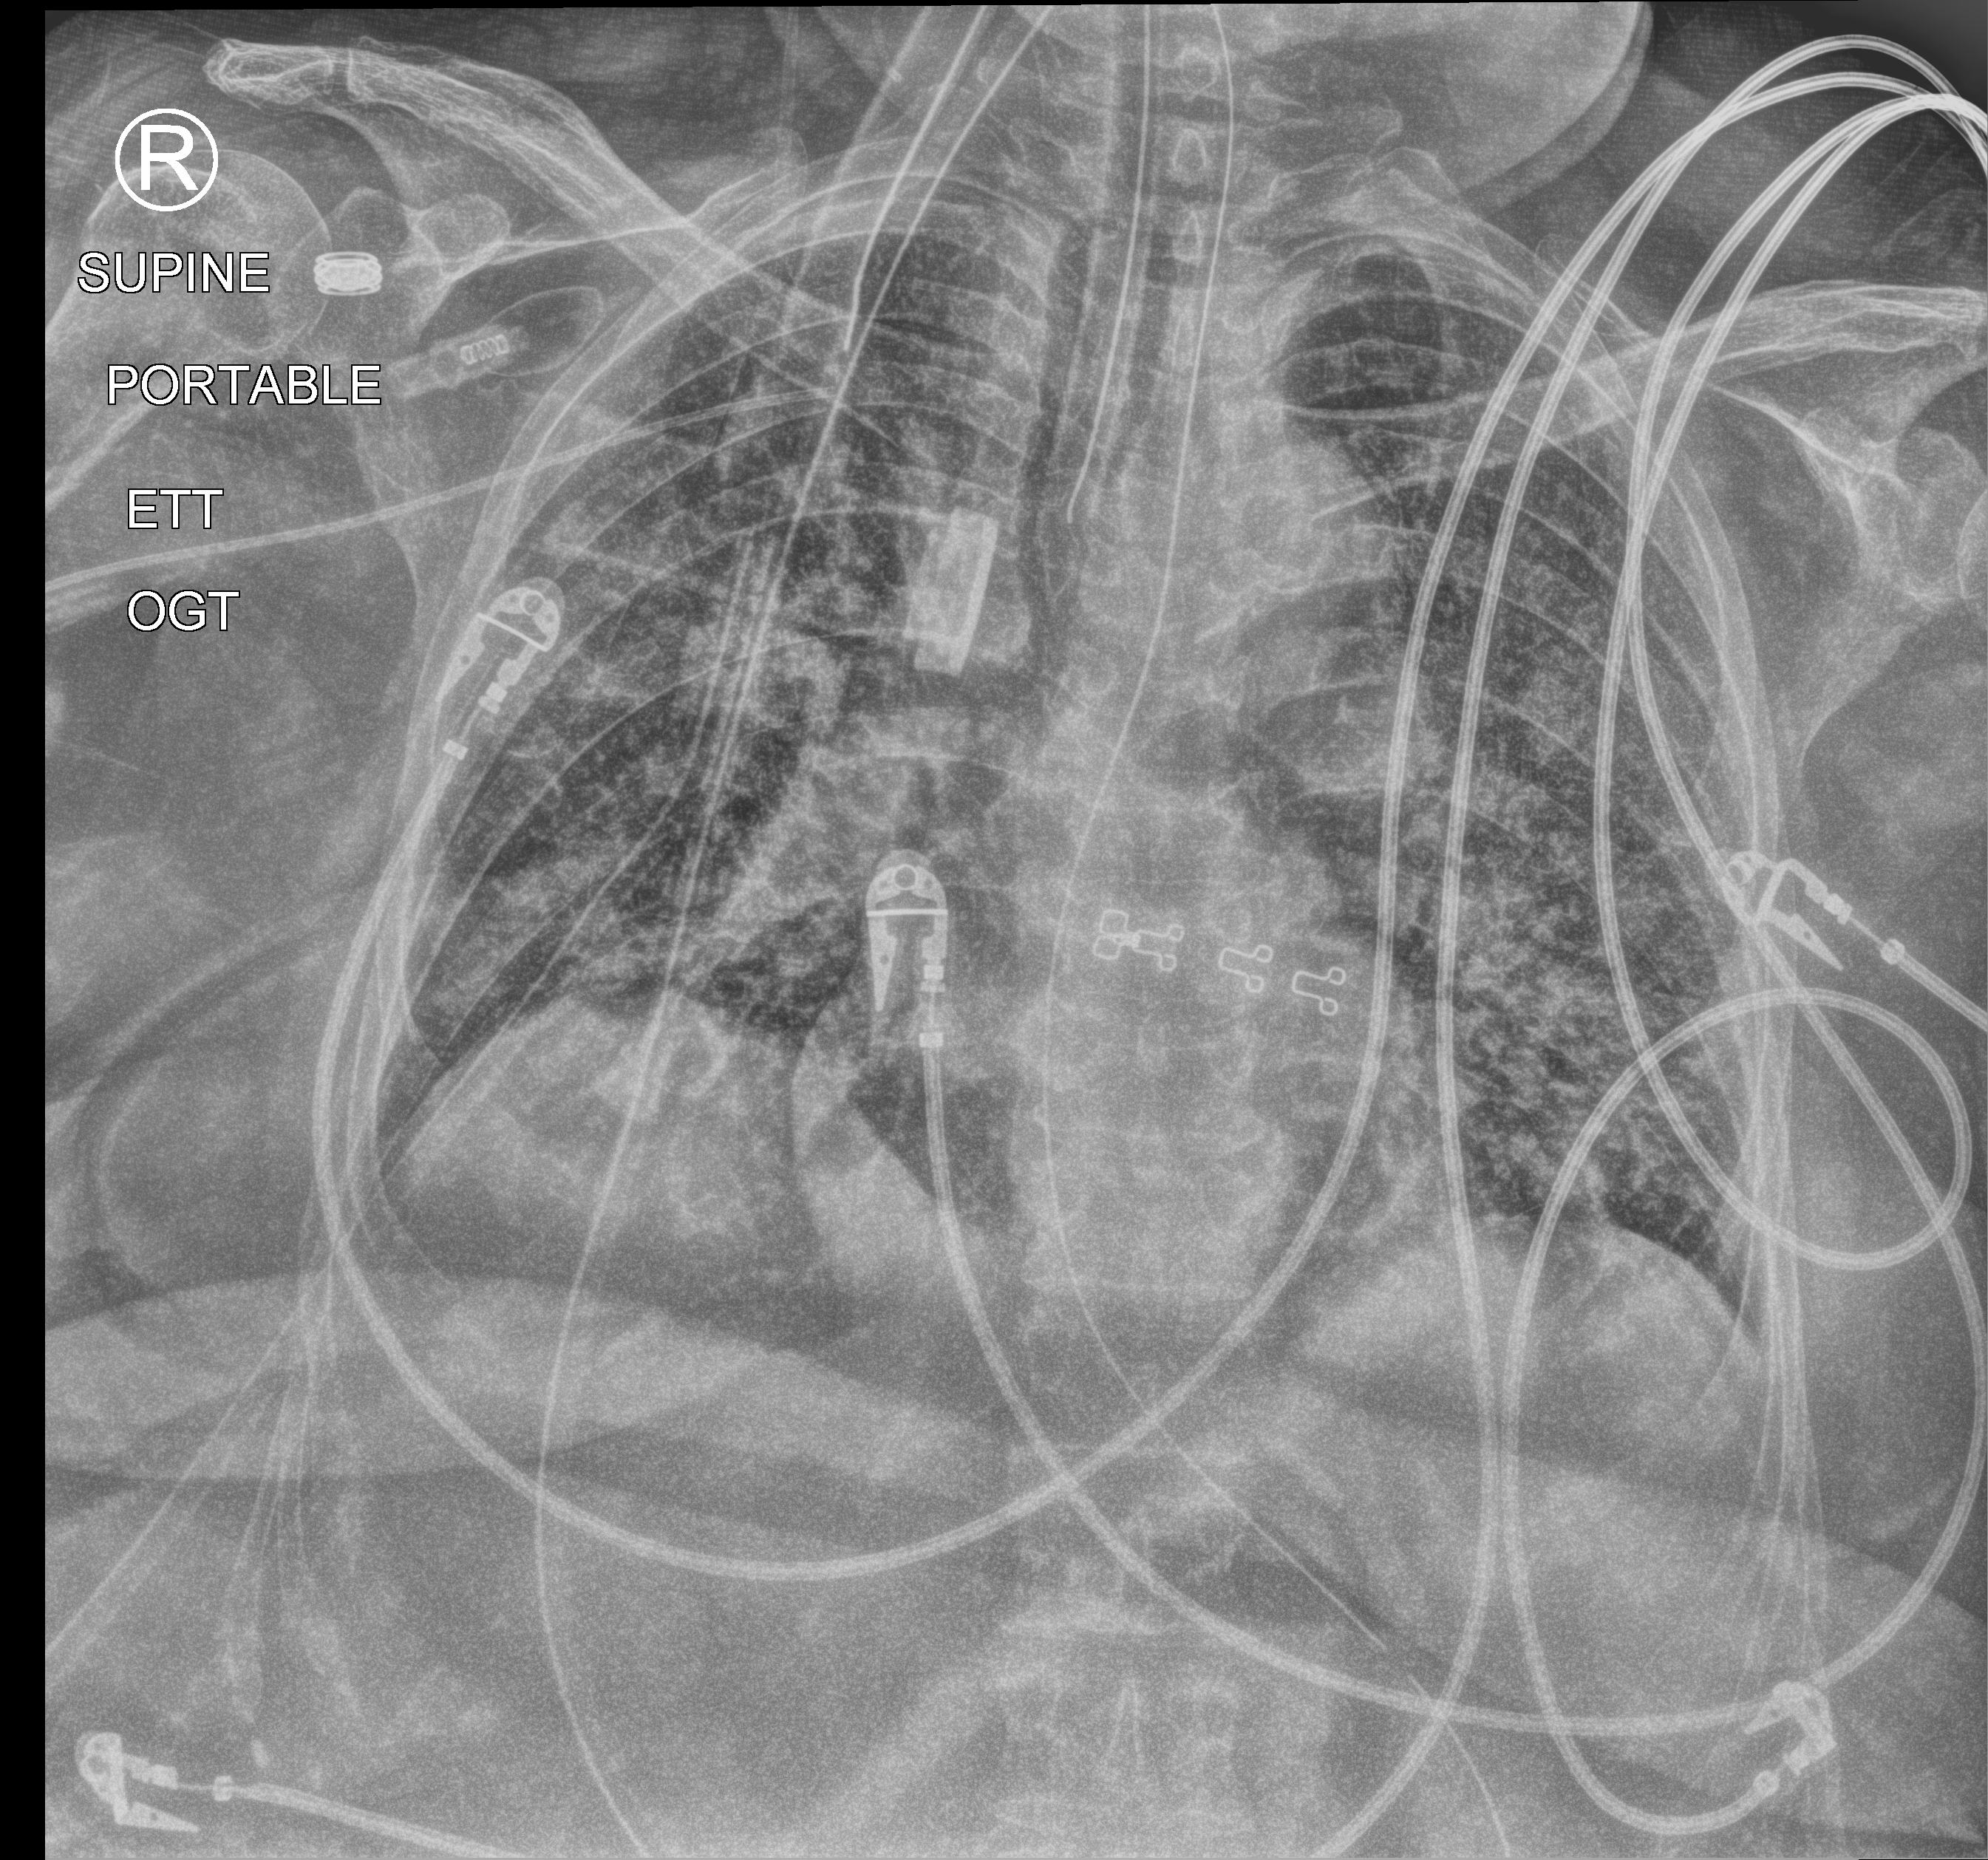
Portable chest radiograph, anteroposterior (AP) projection. Female patient hospitalised with COVID-19, age 60–74 years.
From the hospital-stay record, not from the radiograph (when in the stay this image was taken is not recorded): mechanically ventilated during this hospital stay: yes; admitted to intensive care during this hospital stay: yes; length of hospital stay: 15 days.